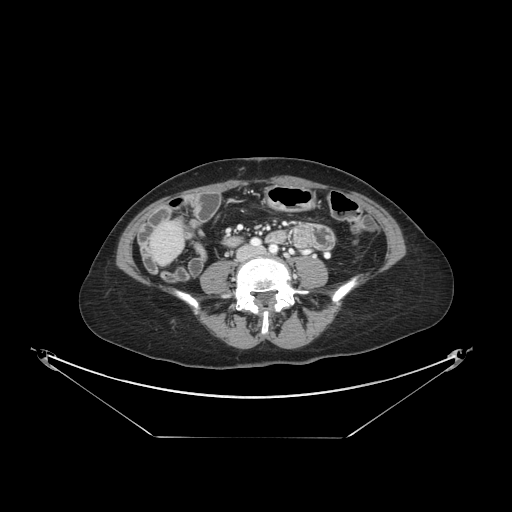
Contrast-enhanced abdominal CT, one axial slice. Position 21 of 148 along the scan axis. Intravenous contrast given. Soft-tissue window (W 400 / L 40 HU). 2.5 mm slice thickness. 512 × 512 image matrix, field of view 500 × 500 mm. Female patient, age 73 years. From the clinical record (not read from this slice): diagnosis: colorectal cancer liver metastases, imaged before liver resection; multiple liver metastases: no; largest metastasis: 1 cm; disease in both lobes: no.
Structures marked on this image (manually delineated by an expert):
- liver: bounding box <153,224,182,262> (left, top, right, bottom; pixels)